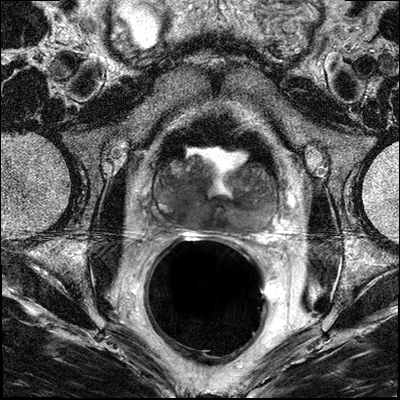
Multiparametric prostate MRI examination; 3 images, each a single mid-volume slice chosen by position (not for content). Treatment context recorded for this patient: No surgery, his oncology plan was to start definitive external beam radiation theraphy and ADT.
Image 1: T2-weighted axial slice, slice 17 of 32.
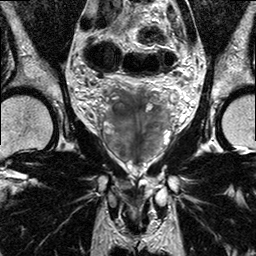
Image 2: coronal T2-weighted image, slice 13 of 24.
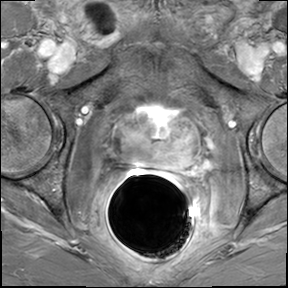
Image 3: DCE (dynamic gadolinium-enhanced) axial slice, slice 17 of 32, dynamic phase 5 of 8.
Report of this MRI examination:
prostate has a maximal lateral diameter of 5.2 cm, a maximal craniocaudal diameter of 5.2 cm and a maximal AP diameter of 3.0 cm resulting in an estimated gland volume of 42 cc. Status post TURP. Due to expected TURP changes the zonal anatomy not preserved. There is a bilateral tumor seen in the left and right posterior peripheral zone from with measuring in its max. extension approx. 4.0 x 2.0 cm (the dominant mass in the upper third/base from 4-8 o'clock) (Image 20 series 501). There is tumor extension involving midthird and apical third (all three levels are involved bilaterally). No evidence for involvement of the neurovascular bundle on either side. There is seminal vesicles infiltration (bilateral the seminal vesicle base is infiltrated (Images 22-24 series 501. Image 15 series 401). No manifest involvement of bladder neck (slightly obscured due to TURP changes. No involvement of rectal wall. No suspiciously enlarged obturator and iliac lymph nodes. IMPRESSION: 1) Bilateral prostate cancer with seminal vesicles infiltration. 2) The dominant mass measures 4.0 x 2.0 cm, located in left and right posterior peripheral zones of the prostate base. The tumor extents from base, through midthird into the apex and infiltrates the seminal vesicles infiltration. 3) No manifest involvement of bladder neck (slightly obscured due to TURP changes). 4) No involvement of rectal wall. 5) No suspiciously enlarged obturator or iliac lymph nodes. 6) St. post TURP, with expected defect.

Prostate biopsy pathology (as recorded):
Gross Description The specimen consists of multiple core fragments of tan soft tissue measuring 0.3cm to 1.8cm in length and 0.1cm in diameter. The specimen is submitted in six cassettes.1-right pz, 2-right pz/tz, 3-right apex, 4-left pz, 5-left pz/tz, 6-left apex. PROSTATE 1. RIGHT PZ: PROSTATIC ADENOCARCINOMA, GLEASON SCORE 4+3=7/10, INVOLVING TWO OF TWO CORES AND 20% OF TOTAL TISSUE. PERINEURAL INVASION SEEN. 2. RIGHT PZ/TZ: PROSTATIC ADENOCARCINOMA, GLEASON SCORE 4+3=7/10, INVOLVING TWO OF TWO CORES AND 90% OF TOTAL TISSUE. PERINEURAL INVASION SEEN. 3. RIGHT APEX: PROSTATIC ADENOCARCINOMA, GLEASON SCORE 4+4=8/10, INVOLVING ONE OF ONE CORE AND 95% OF TOTAL TISSUE. 4. LEFT PZ: PROSTATIC ADENOCARCINOMA, GLEASON SCORE 3+3=6/10, INVOLVING TWO OF MULTIPLE CORES AND 5% OF TOTAL TISSUE. PERINEURAL INVASION SEEN. 5. LEFT PZ/TZ: PROSTATIC ADENOCARCINOMA, GLEASON SCORE 4+3=7/10, INVOLVING TWO OF TWO CORES AND 50% OF TOTAL TISSUE. 6. LEFT APEX: PROSTATIC ADENOCARCINOMA, GLEASON SCORE 3+3=6/10, INVOLVING ONE OF ONE CORE AND 20% OF TOTAL TISSUE.